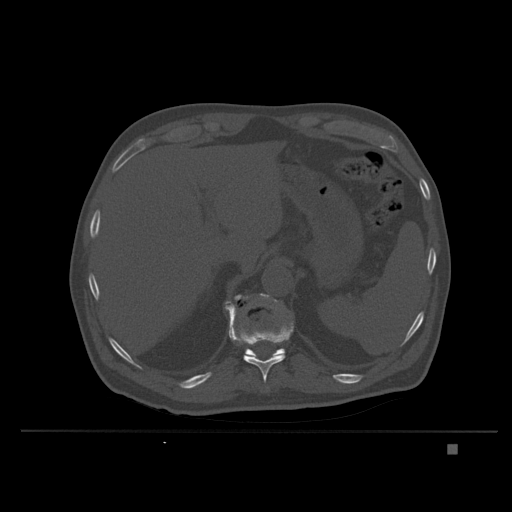
CT including the spine, one axial slice; slice 172 of 435 in the series (ordered by position); bone window (W 1800 / L 400 HU); 1.5 mm slice thickness; 512 × 512 image matrix. Patient: male, 73 years. Case-level facts recorded for this patient, not image findings: primary cancer: skin.
Annotated regions visible in this slice (semi-automatically segmented with operator editing):
- T11 vertebra: bounding box <227,305,293,382> (left, top, right, bottom; pixels)
- T12 vertebra: <226,295,285,357>